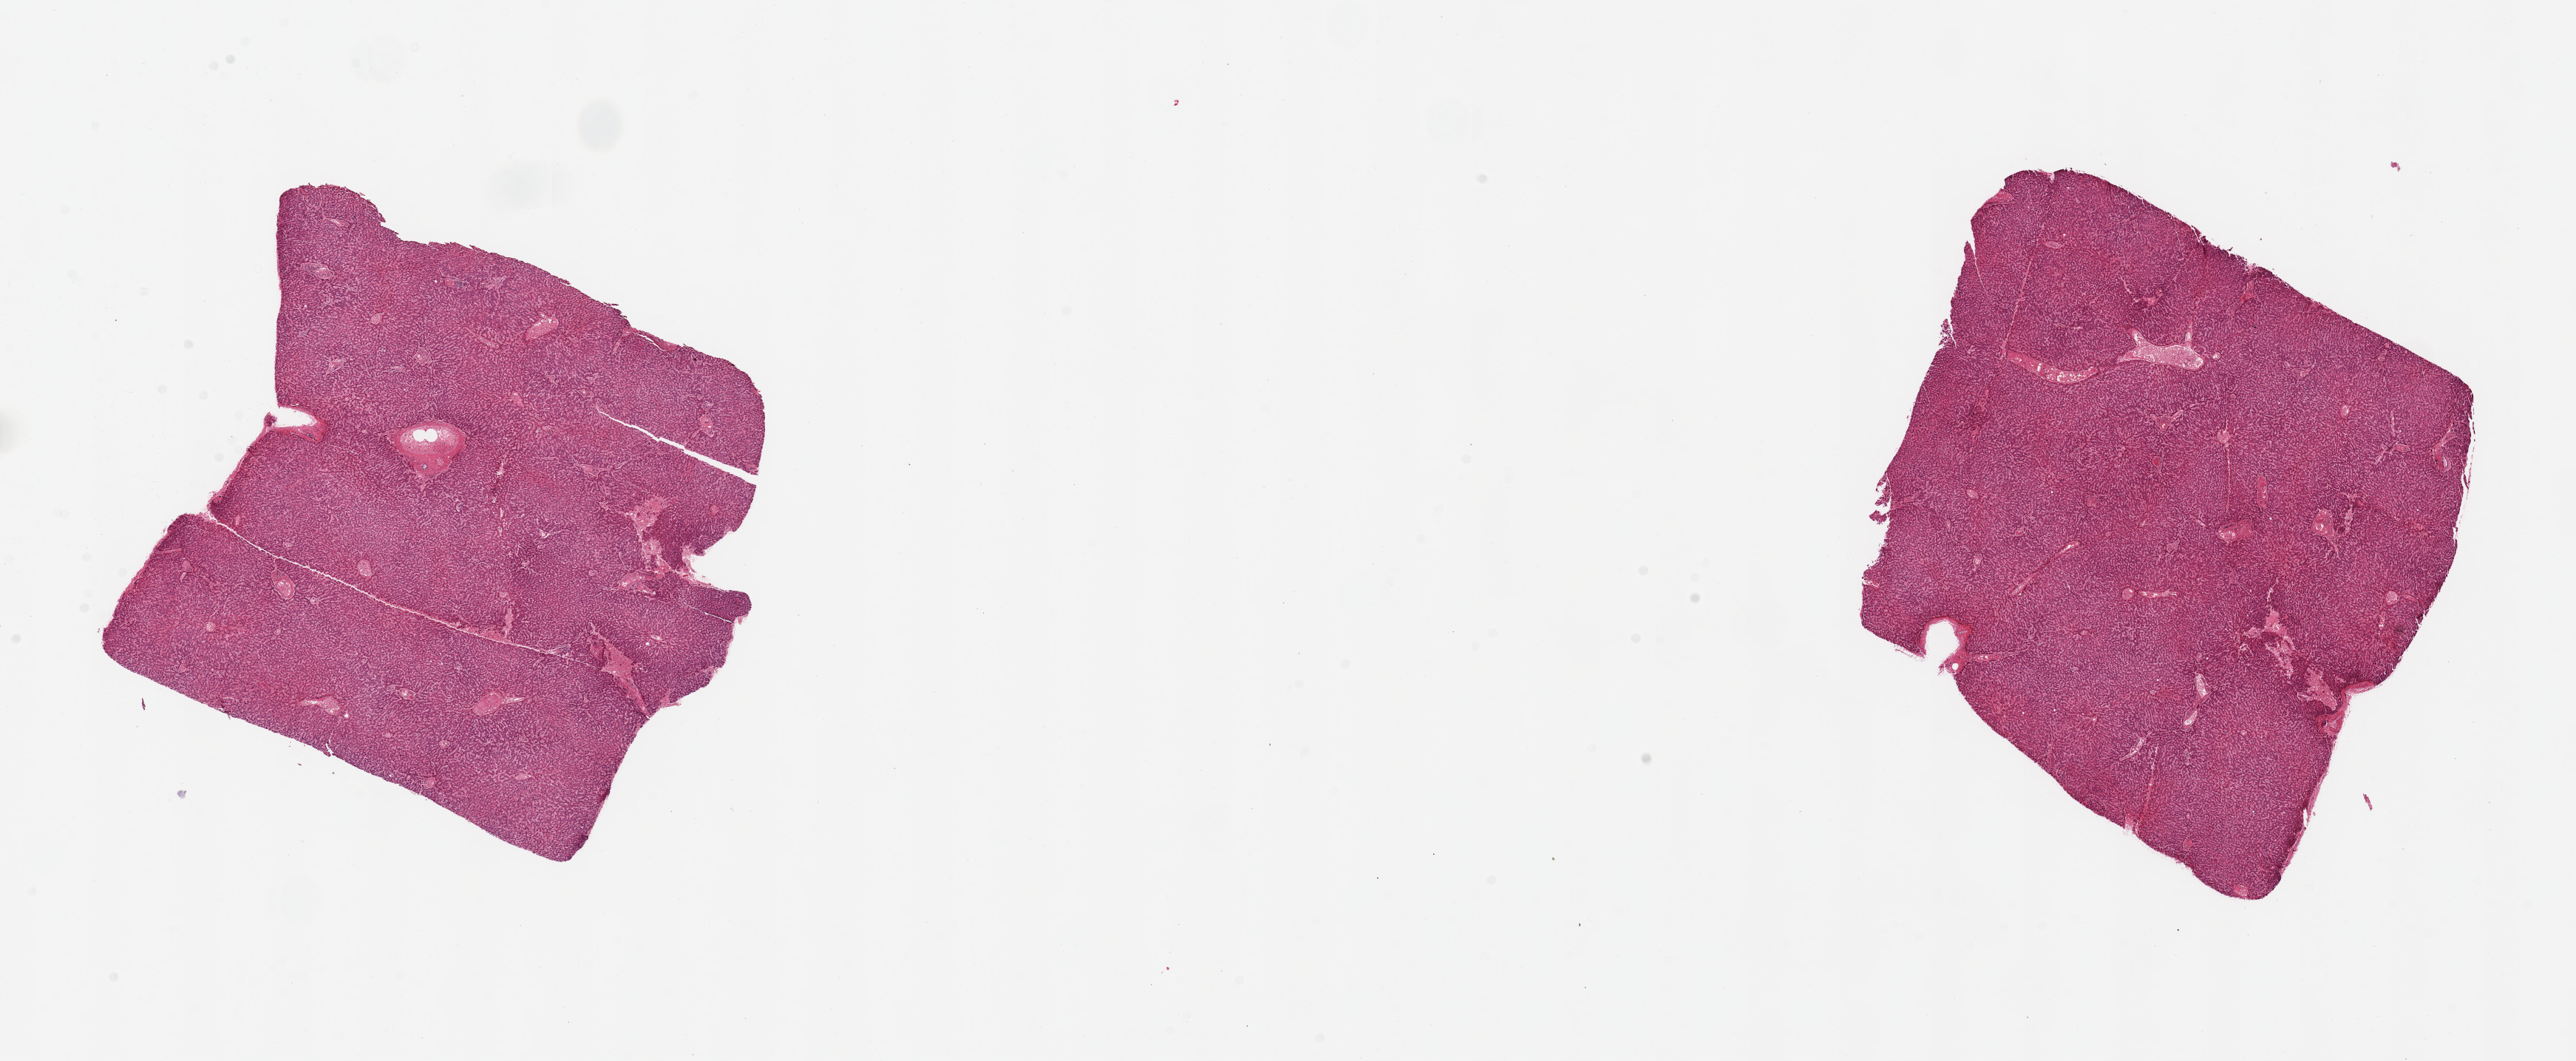
Digitized H&E-stained section, a low-resolution overview of the entire scanned area, about 27.6 x 11.3 mm, PAXgene-fixed, paraffin-embedded tissue, target tissue: liver, tissue donor sample. Donor: male.
* pathologist's review note for this sample: 2 pieces, 6.5x6 & 6x6mm; no lesions